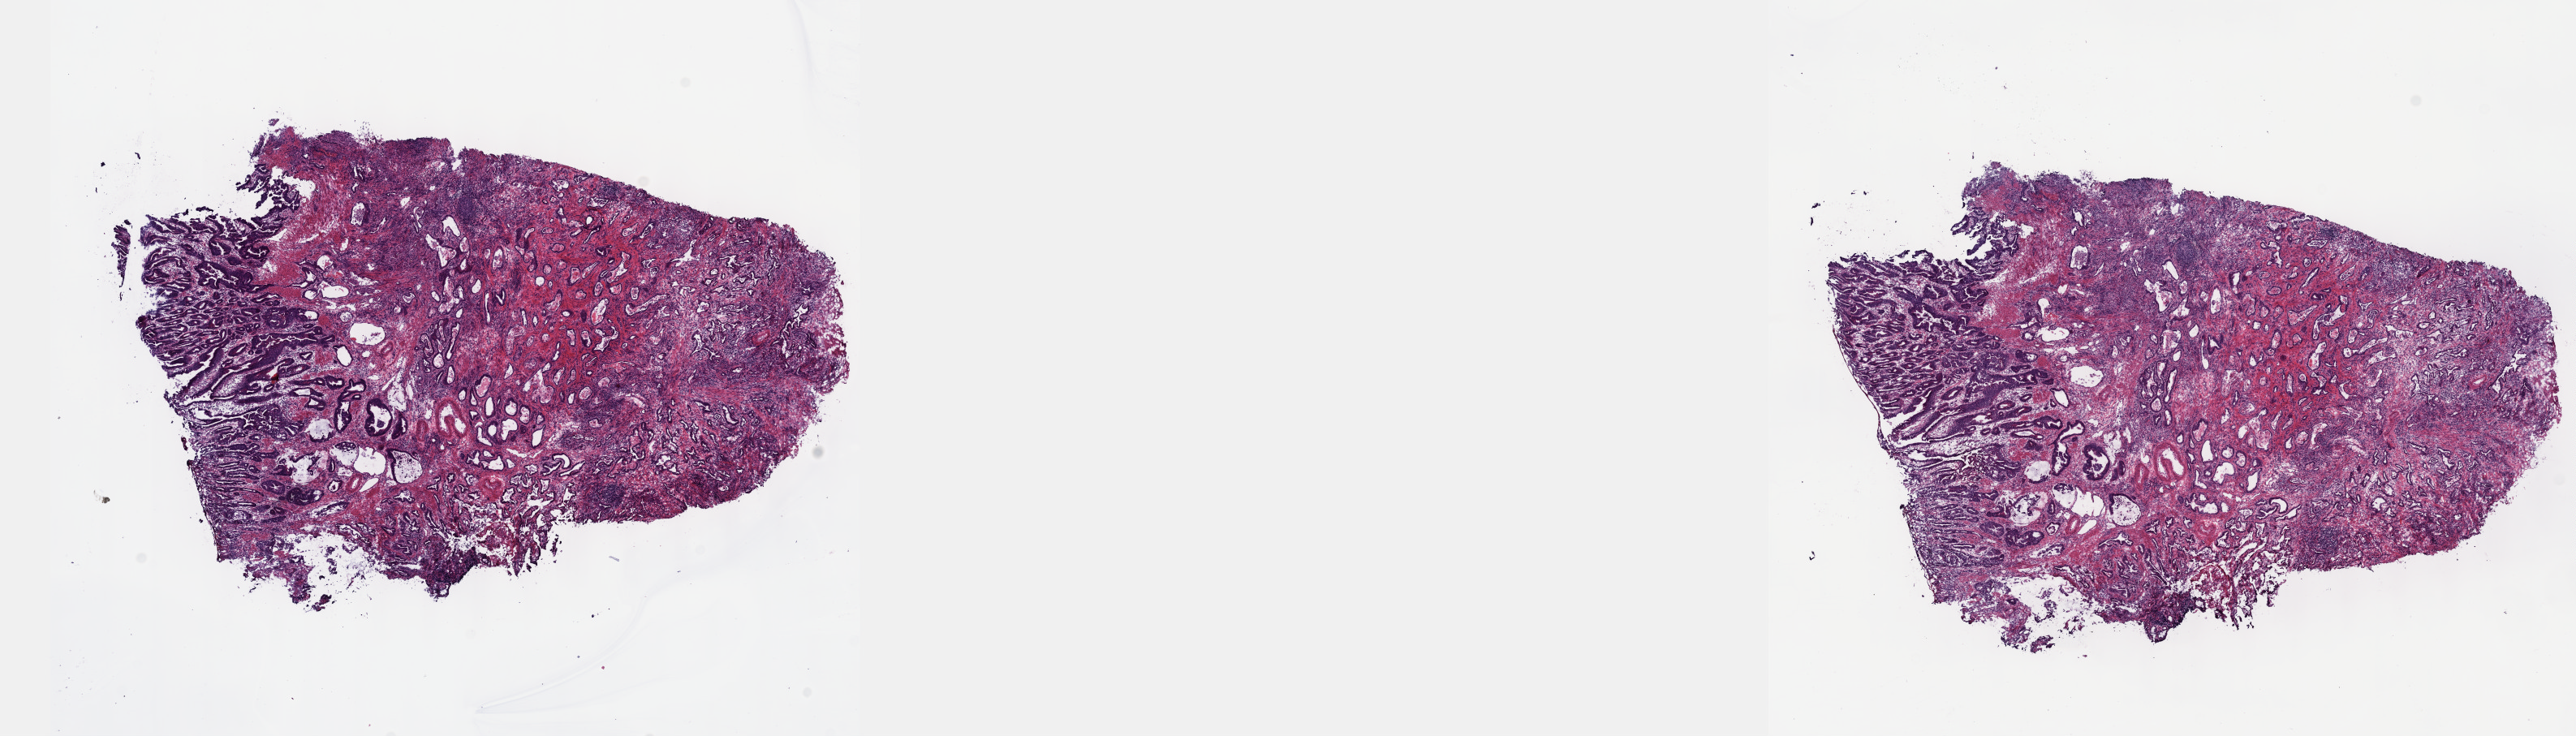
Digitized H&E-stained tissue section (whole slide), shown as a low-resolution overview of the whole scanned area (about 25.7 x 7.3 mm, acquisition: 40x scan). Frozen section from the top of the tissue portion. Primary tumour sample from the esophagus. Male, age 77 years at initial diagnosis.
Pathologic diagnosis: Adenocarcinoma, NOS (lower third of esophagus).